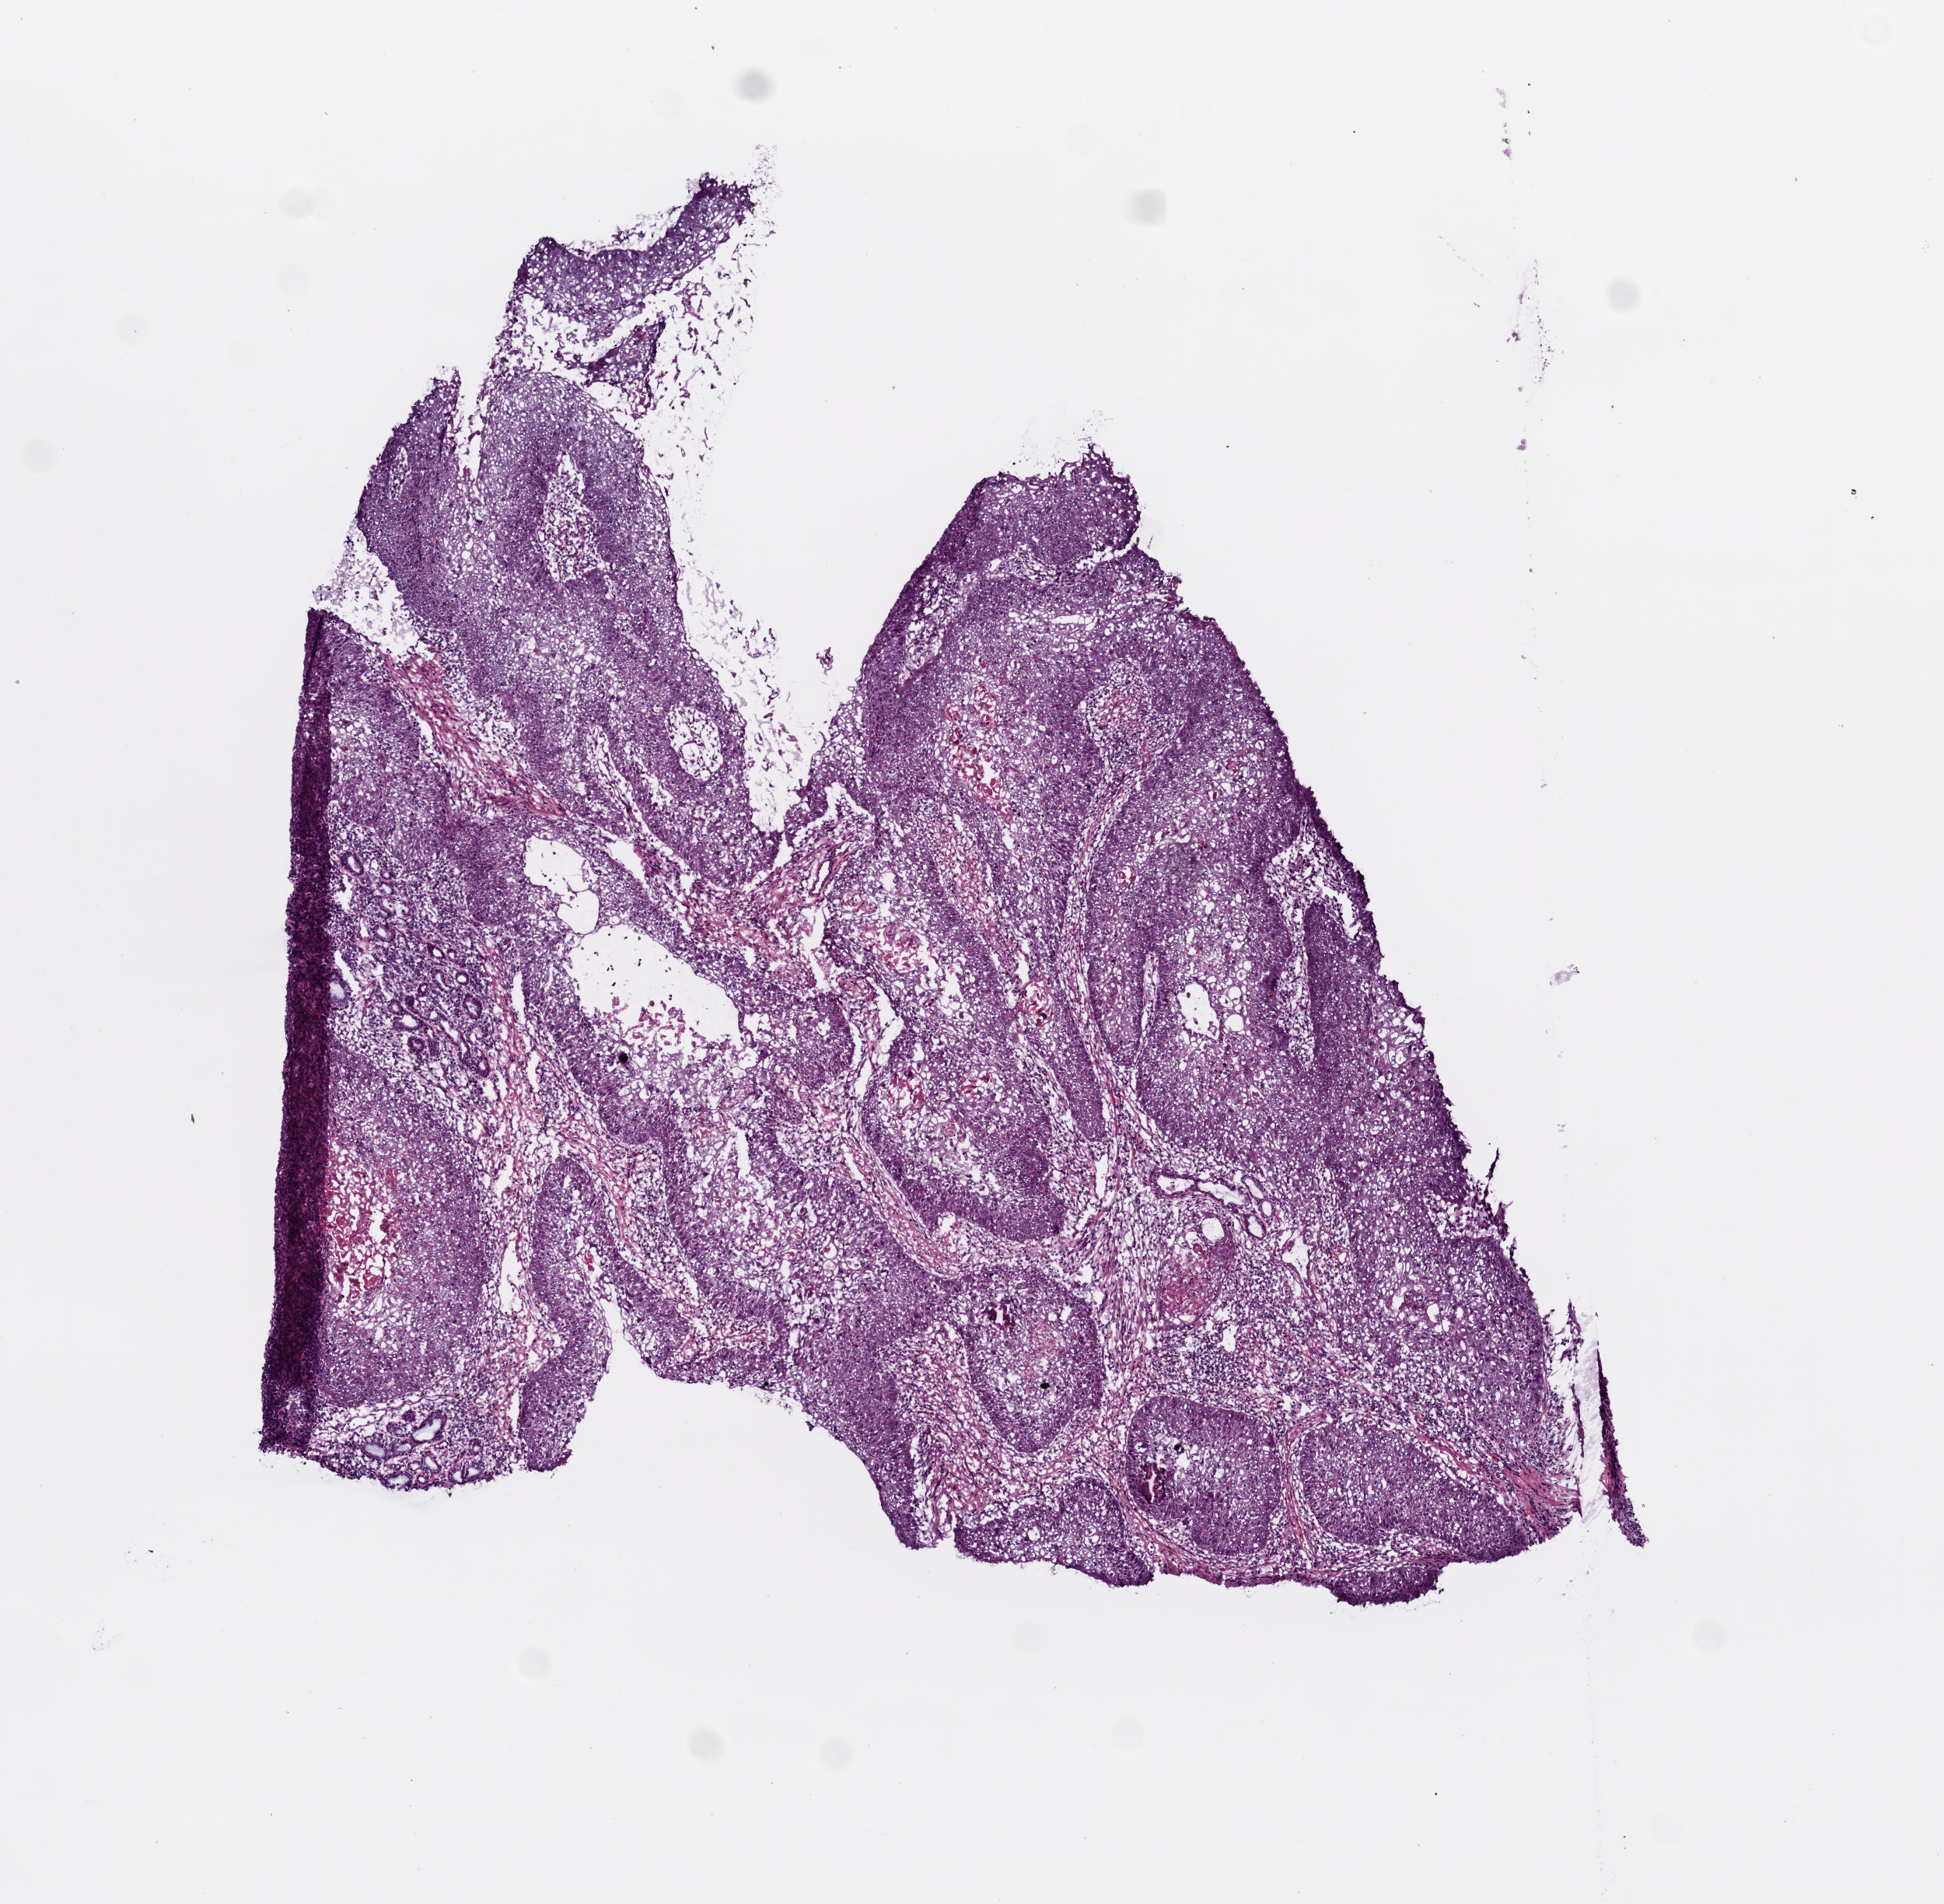
Whole-slide histology image, Hematoxylin and eosin (H&E) stained — a low-resolution overview of the entire scanned area, about 5.0 x 4.9 mm; frozen section; head and neck, primary tumour sample. Male, age 54 years at initial diagnosis. Histologic grade: G2 (moderately differentiated). Composition of this section per pathologist review: tumour cells 80%, tumour nuclei 80%, normal cells 0%, stromal cells 15%, necrosis 5%.
* AJCC pathologic stage: IVA (7th edition)
* pathologic diagnosis: Squamous cell carcinoma, NOS (larynx, NOS)
* lymph nodes positive (case pathology): 1 of 68 examined
* laterality: right
* TNM: T3 N2c